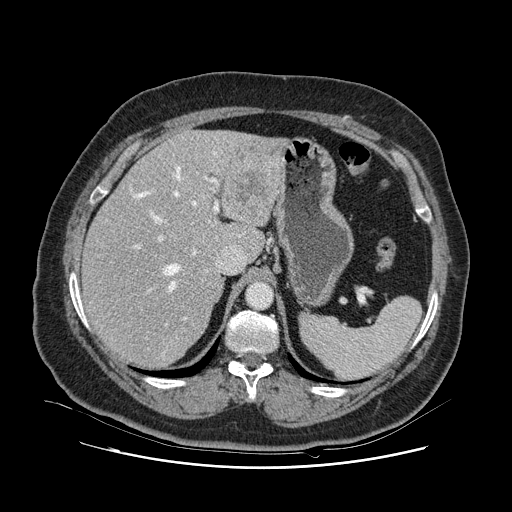
Contrast-enhanced abdominal CT, one axial slice; slice 80 of 132 in the series (ordered by position); 120 kVp; intravenous contrast given; soft-tissue window (W 400 / L 40 HU); 2.5 mm slice thickness; 512 × 512 image matrix, field of view 391 × 391 mm. Female patient, age 73 years. From the clinical record (not read from this slice): diagnosis: colorectal cancer liver metastases, imaged before liver resection; multiple liver metastases: no; largest metastasis: 7 cm; disease in both lobes: no.
Structures marked on this image (outlined manually by an expert reader):
- hepatic veins: bounding box <133,152,241,351> (left, top, right, bottom; pixels)
- liver: <83,131,279,365>
- planned liver remnant (the part of the liver to remain after resection): <83,160,238,366>
- portal vein (with intrahepatic branches): <134,173,219,326>
- liver metastasis: <233,164,270,217>